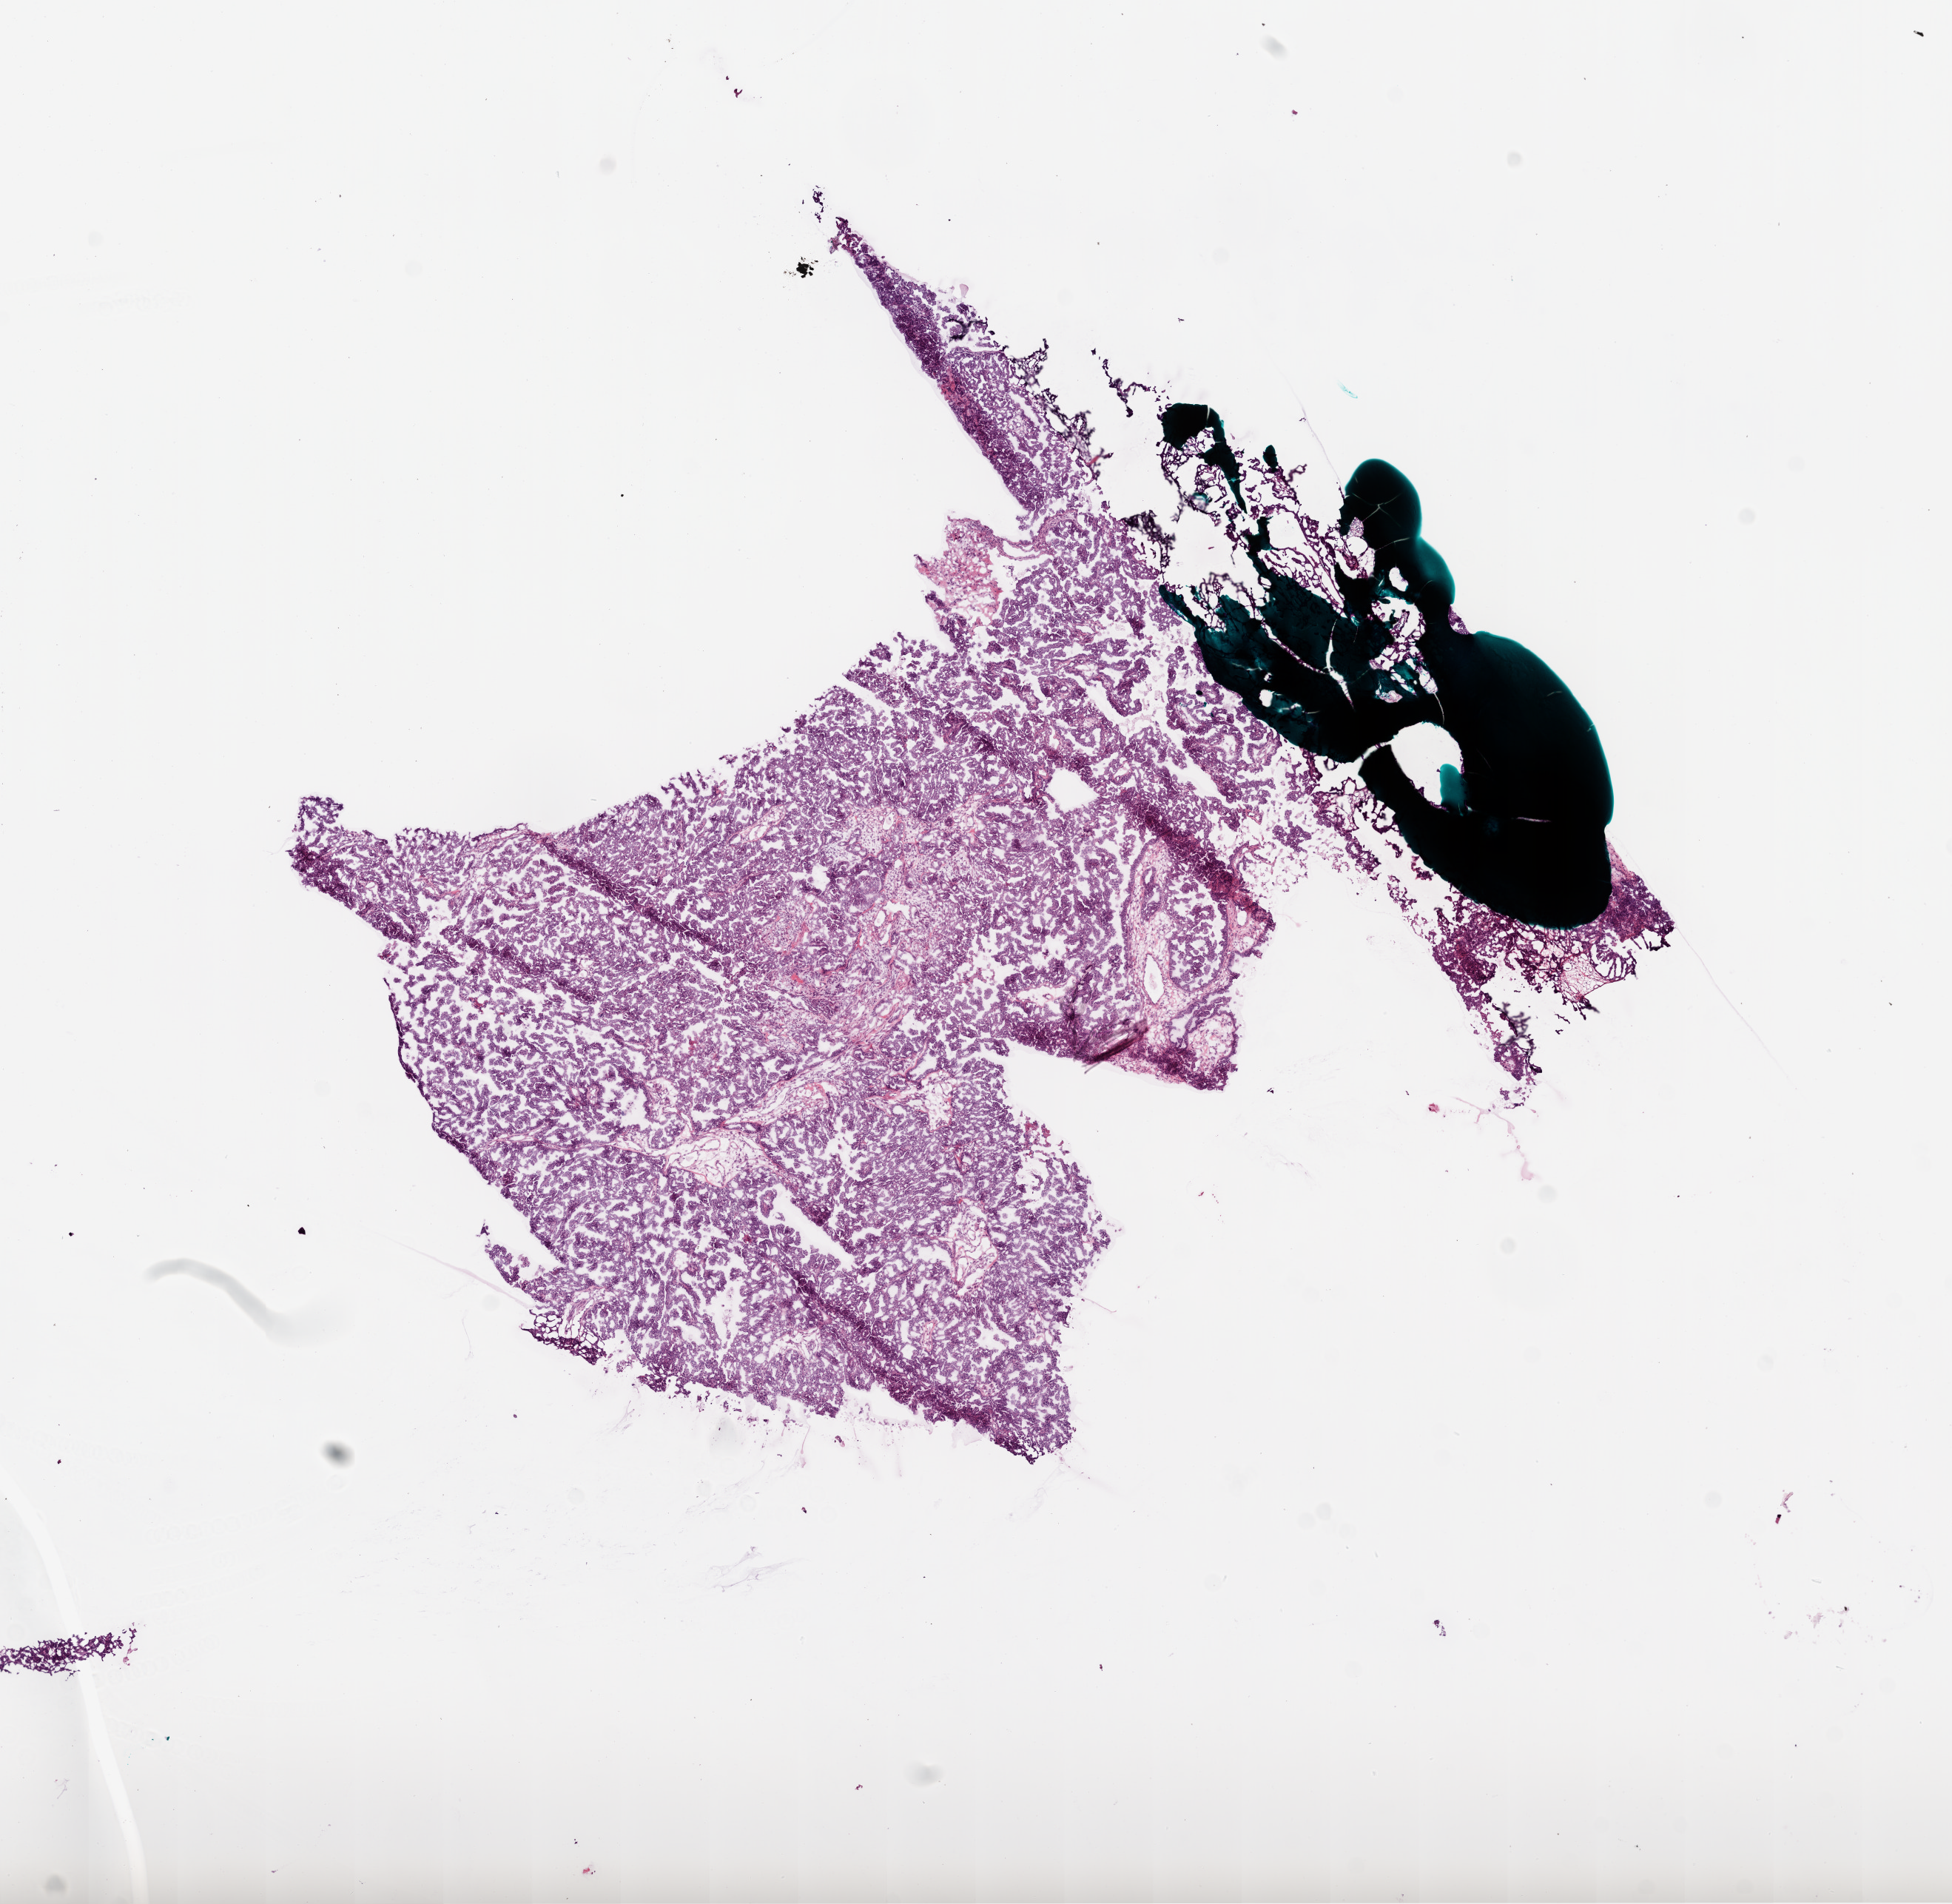
H&E whole-slide image — low-resolution overview of the scanned area, about 10.6 x 10.4 mm (acquisition: 20x scan). Frozen section from the bottom of the tissue portion. Sample: primary tumour, ovary. Female, age 71 years at initial diagnosis. Histologic grade: G3 (poorly differentiated). Pathologist review of this section (percent, as recorded): tumour cells 90%, tumour nuclei 95%, normal cells 5%, stromal cells 5%, necrosis 0%.
Histologic diagnosis: Serous cystadenocarcinoma, NOS. FIGO stage: IIIC.